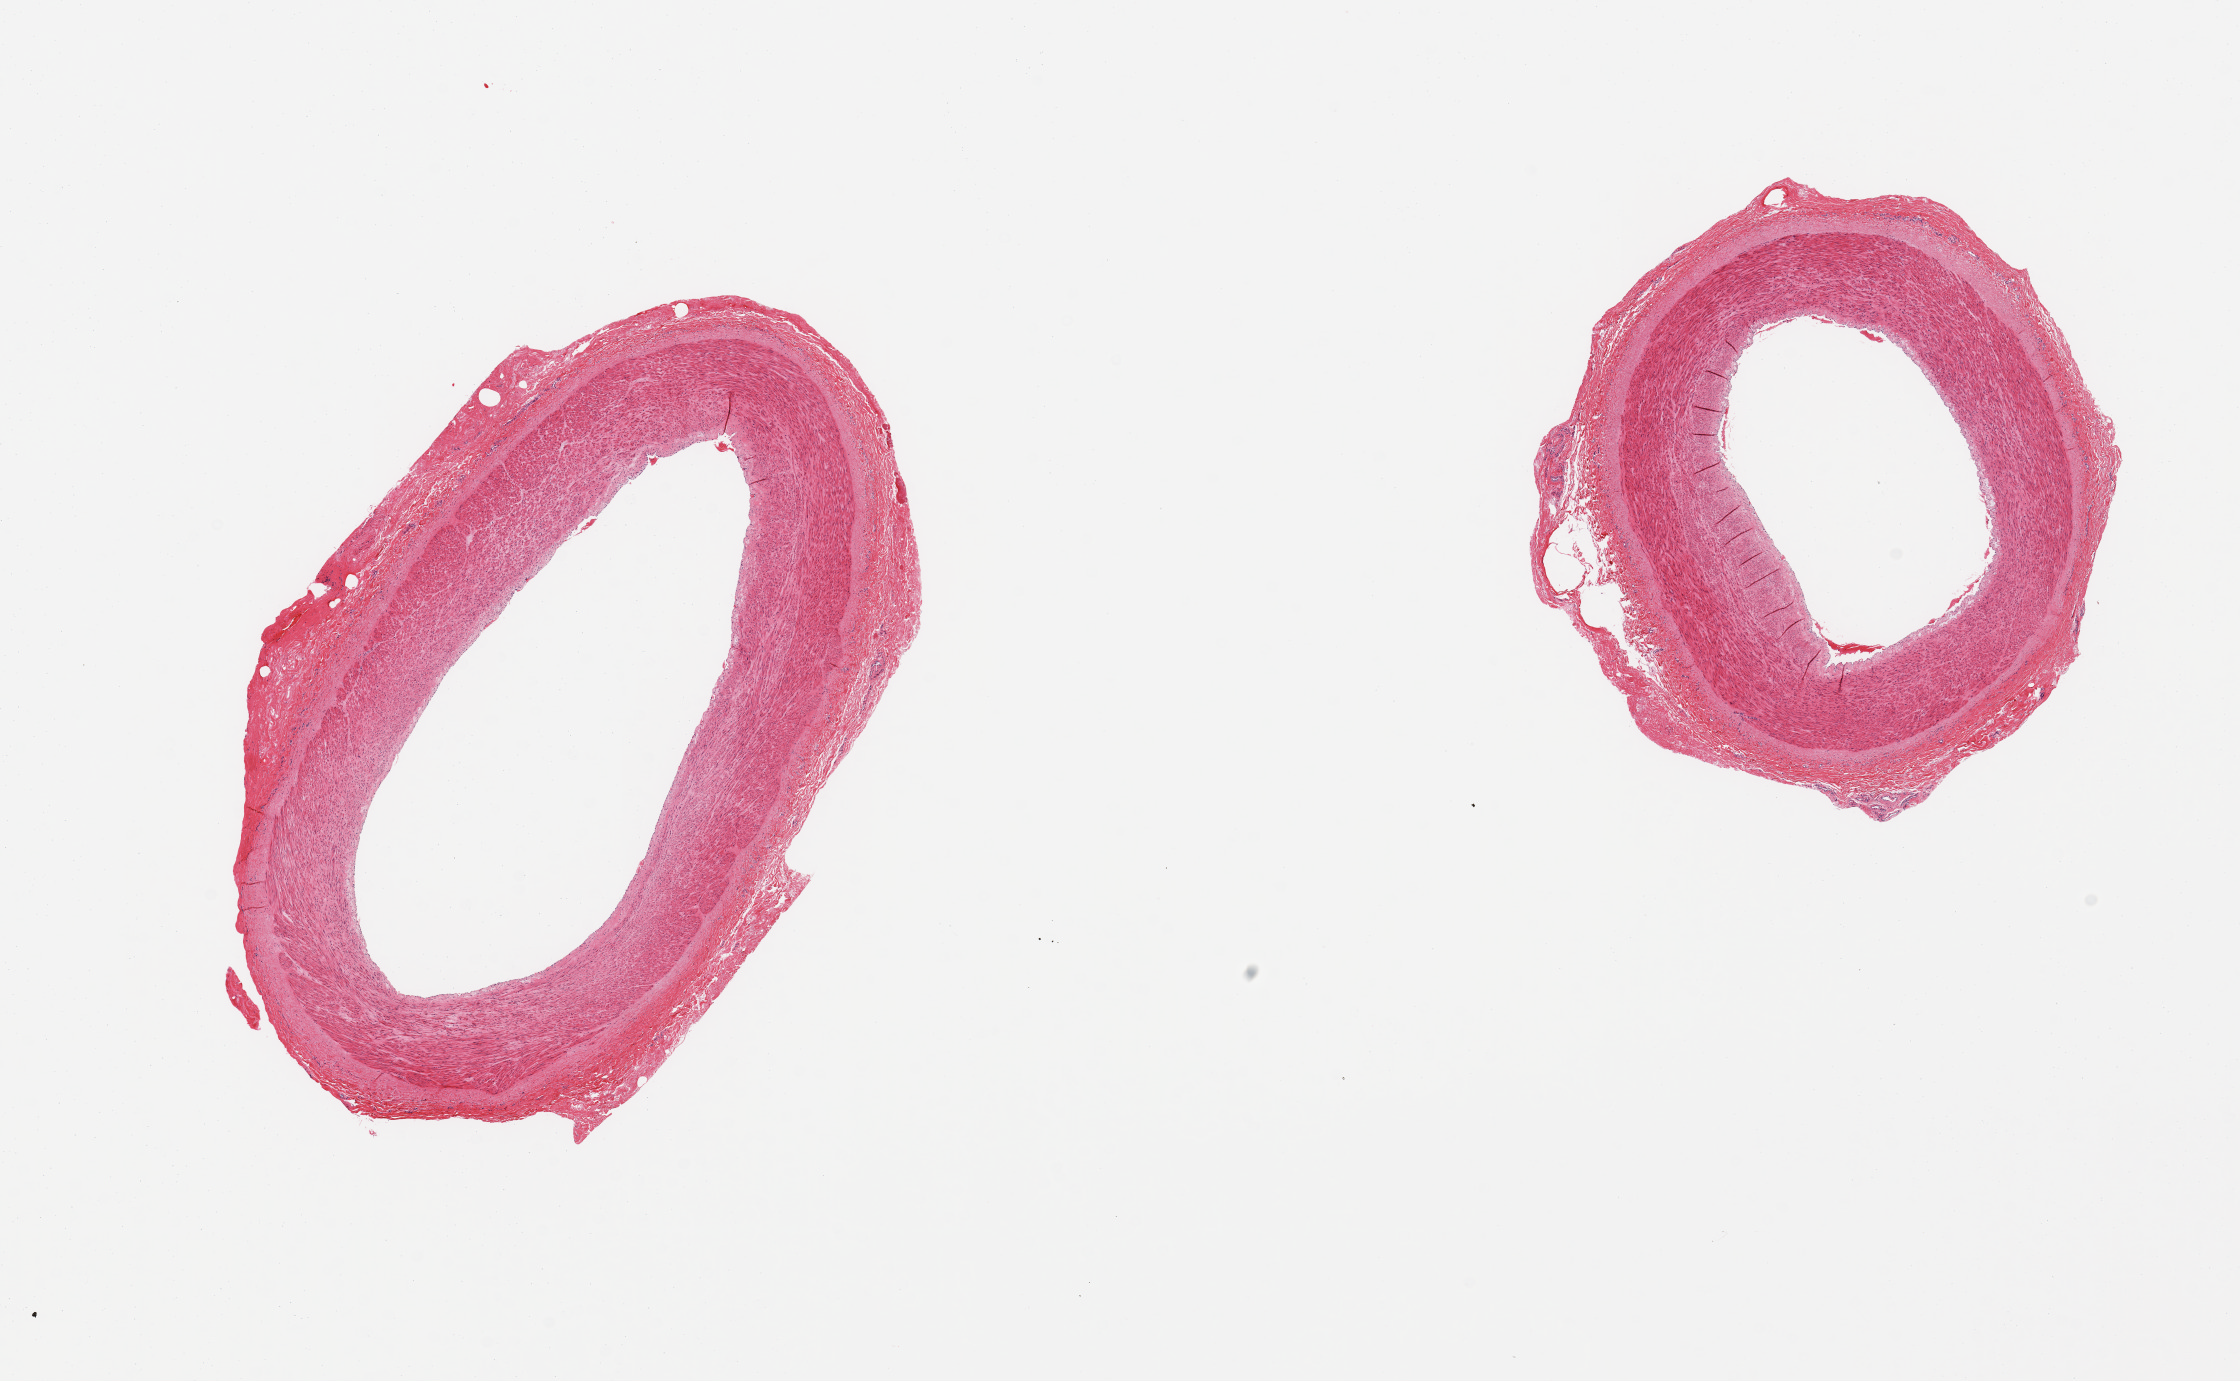
Whole-slide image, haematoxylin and eosin stain, a low-resolution overview of the entire scanned area, about 17.7 x 10.9 mm (acquisition: 20x scan); PAXgene-fixed paraffin-embedded (PFPE) section; target tissue: tibial artery; donor tissue sample. Donor sex: male.
Reviewer comment on this tissue sample: 2 pieces, no atherosis/adherent fat.